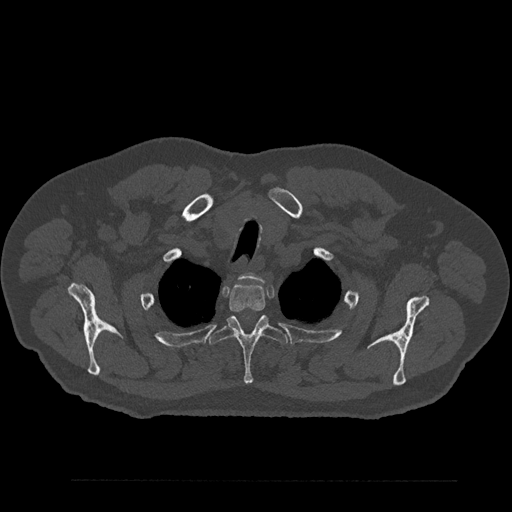
CT including the spine, one axial slice; reconstruction kernel Br40s/3; 120 kVp; bone window (W 1800 / L 400 HU); 512 × 512 image matrix, field of view 430 × 430 mm. Patient: male, 61 years. From the clinical record (not read from this slice): primary cancer: prostate.
Structures marked on this image (semi-automatic segmentation, software-assisted and operator-edited):
- T1 vertebra: bounding box [x1, y1, x2, y2] px = [240, 273, 260, 279]
- T2 vertebra: [228, 282, 266, 313]
- T3 vertebra: [209, 315, 288, 385]